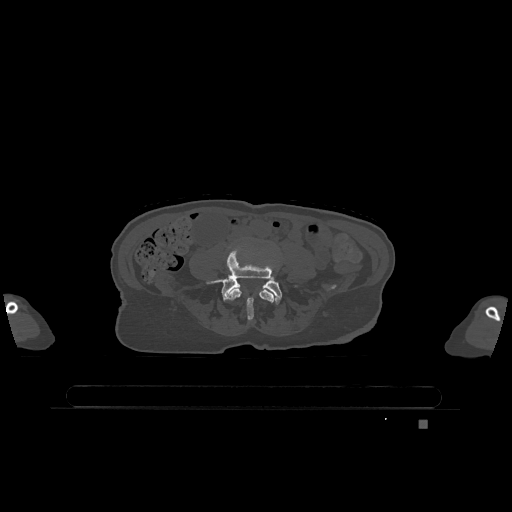
CT including the spine, one axial slice; slice 264 of 1317 in the series (ordered by position); bone window (W 1800 / L 400 HU); 0.5 mm slice thickness; 512 × 512 image matrix, field of view 500 × 500 mm. Patient: female, 74 years. Case-level facts recorded for this patient, not image findings: primary cancer: lung; vertebrae with lytic lesions (as recorded): T1, T4, T5, T6, L4, L5.
Structures marked on this image (semi-automatic segmentation, software-assisted and operator-edited):
- L4 vertebra: bounding box [x1, y1, x2, y2] px = [227, 289, 274, 321]
- L5 vertebra: [209, 253, 282, 305]